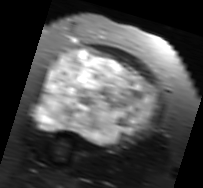
MRI of an extremity soft-tissue mass, one axial slice. Slice 45 of 91 in the series (ordered by position). T2-weighted fat-saturated. MR volume resampled by the dataset authors to the PET/CT grid (not the native acquisition matrix). 3.27 mm slice thickness. 203 × 188 image matrix. Female patient. From the clinical record (not read from this slice): histological type: malignant solitary fibrous tumor; grade: intermediate; site of the primary tumour: right thigh.
Outlined on this slice (expert contour drawn on MRI and transferred to this co-registered scan by the dataset authors):
- gross tumour volume including surrounding oedema: bounding box [x1, y1, x2, y2] px = [30, 47, 159, 146]
- gross tumour volume (mass): [35, 47, 157, 144]